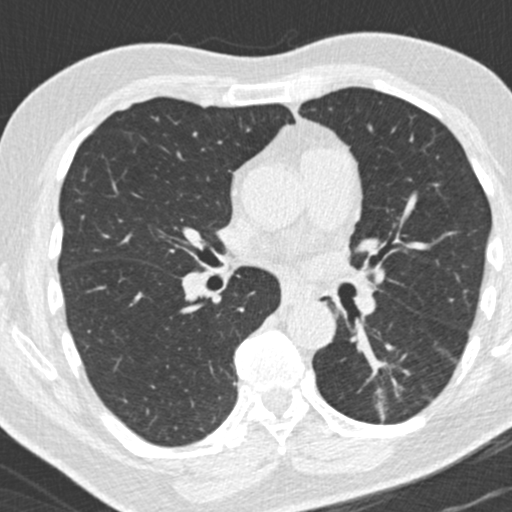
Chest CT (low-dose screening protocol), one axial image, third annual screen, lung window (W 1500 / L -600 HU), standard (soft-tissue) reconstruction kernel (B30f), slice 78 of 180 in the series, 512 × 512 image matrix. Male, age 66 years at enrolment. Former smoker at enrolment.
Lesion marked by an expert reader, bounding box (x1, y1, x2, y2) in pixels: (357, 356, 425, 427). The exam's reader record, not a measurement of the box and not confirmed to be the same lesion: non-calcified nodule or mass ≥4 mm, left lower lobe, 31 × 24 mm, spiculated (stellate) margins, pre-existing on the prior screen: yes; interval growth: yes.